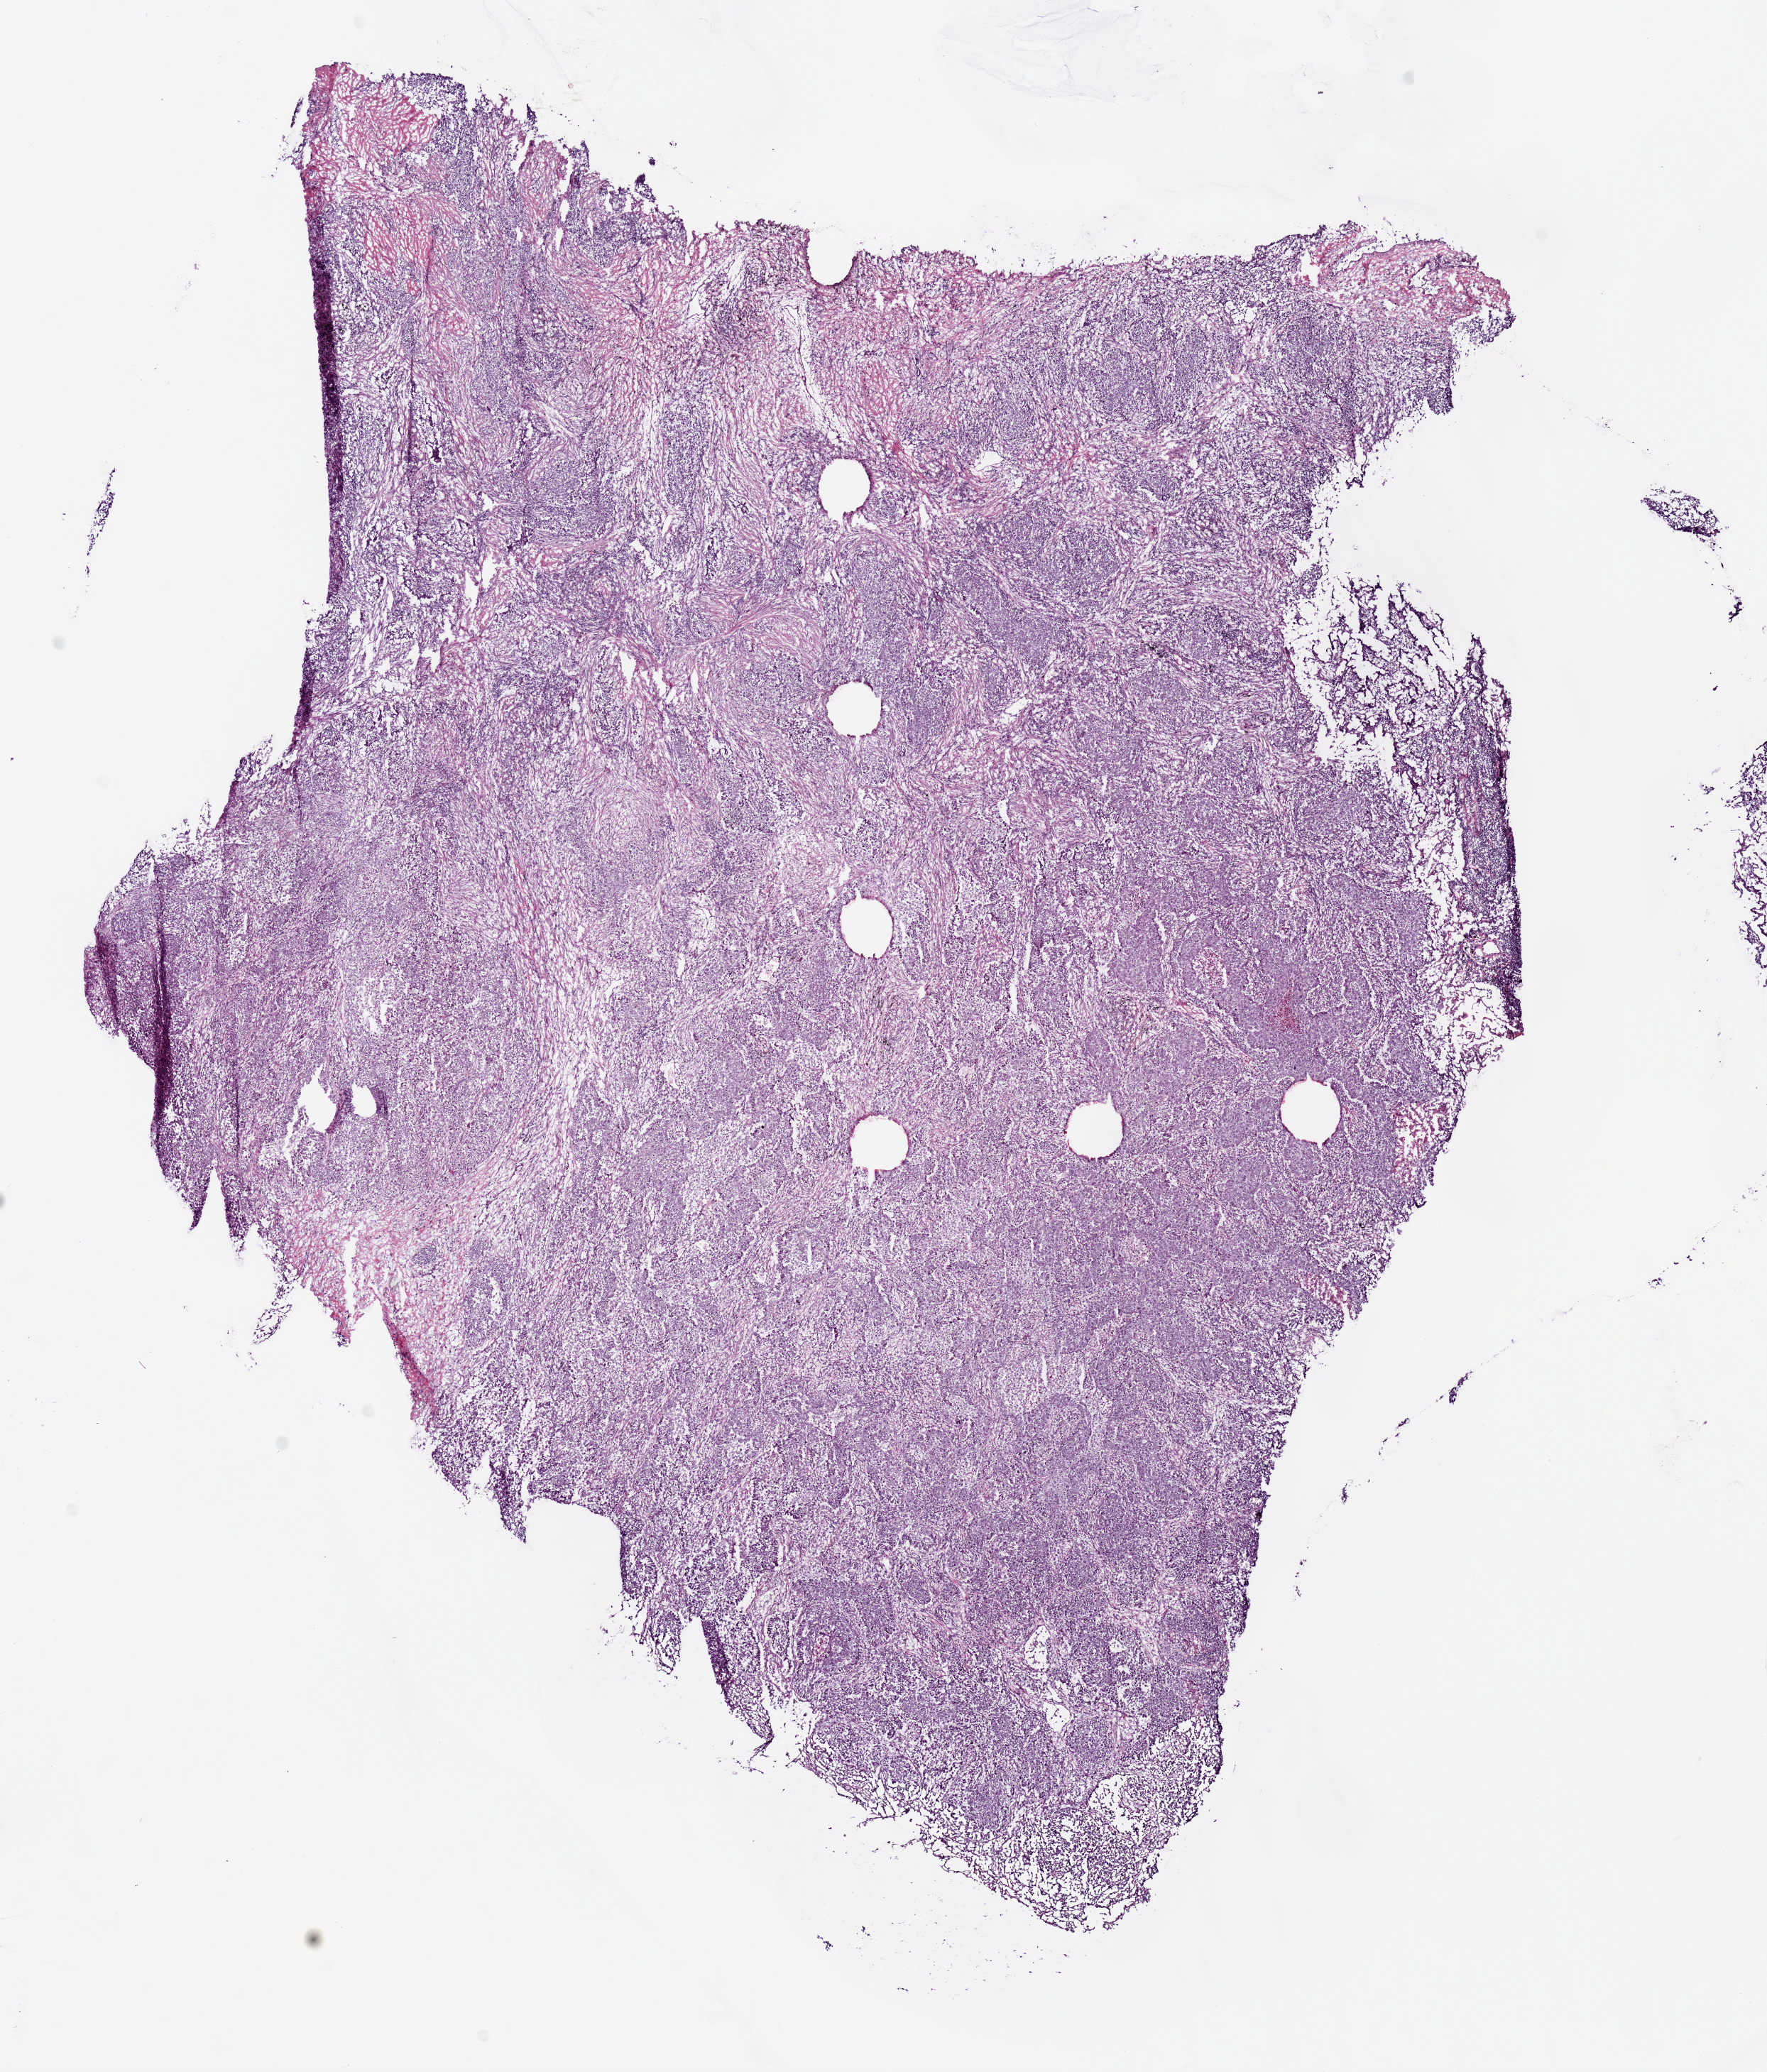
H&E whole-slide image, whole scanned area (about 9.8 x 11.5 mm) shown as a low-resolution overview; frozen section from the top of the tissue portion; primary tumour sample from the lung. Female, age 59 years at initial diagnosis. Slide review estimates, as recorded: tumour cells 80%, tumour nuclei 70%, normal cells 0%, stromal cells 15%, necrosis 5%.
TNM: T2 N1 M0. Laterality: left. AJCC pathologic stage: IIB. Pathologic diagnosis: Adenocarcinoma, NOS (upper lobe, lung).